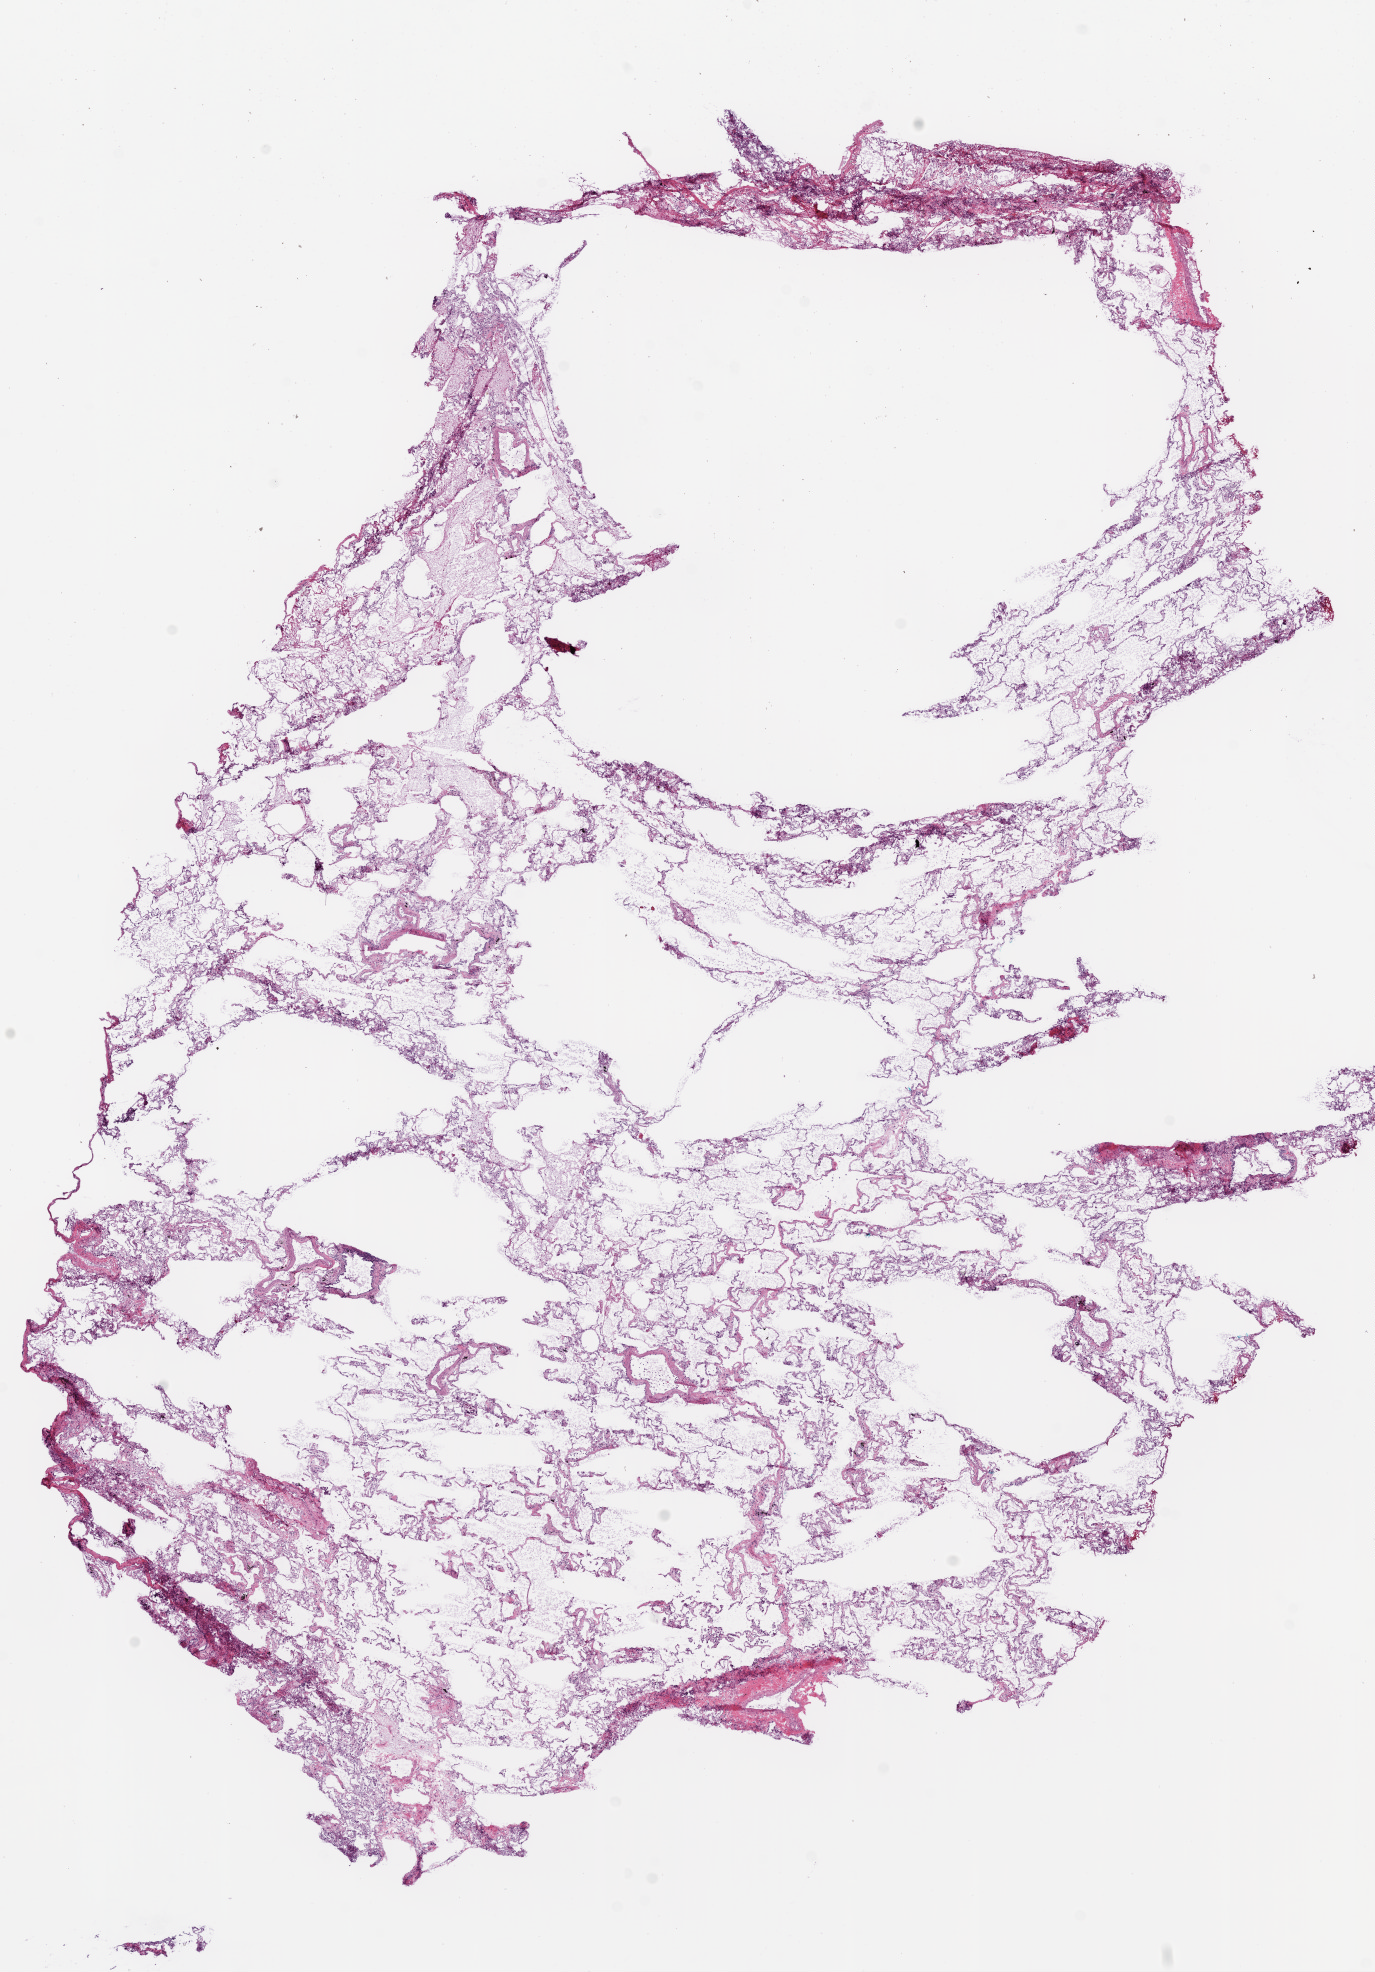
H&E whole-slide image, shown as a low-resolution overview of the whole scanned area (about 11.0 x 15.8 mm, acquisition: 20x scan); frozen section from the bottom of the tissue portion; sample: solid tissue normal (non-tumour tissue), lung. Patient: female, age at initial diagnosis 79 years.
This section: solid tissue normal sample (biorepository sample class). Patient diagnosis: Squamous cell carcinoma, NOS (upper lobe, lung).